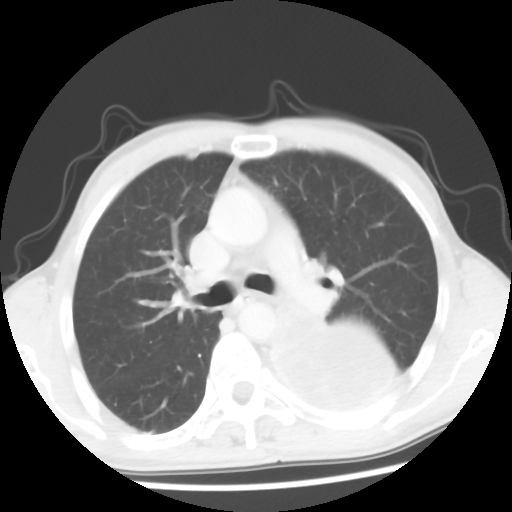
Chest CT, one axial slice. Slice 36 of 56 in the series (ordered by position). Lung window (W 1500 / L -600 HU). 5 mm slice thickness. 512 × 512 image matrix, field of view 318 × 318 mm. Male patient, age 60 years. Case-level facts recorded for this patient, not image findings: clinical TNM (as recorded): T4 N0 M0.
Structures marked on this image (rectangle marked by the reading radiologist):
- lung tumour (recorded histology: squamous cell carcinoma): box from (x=254, y=312) to (x=422, y=431) px